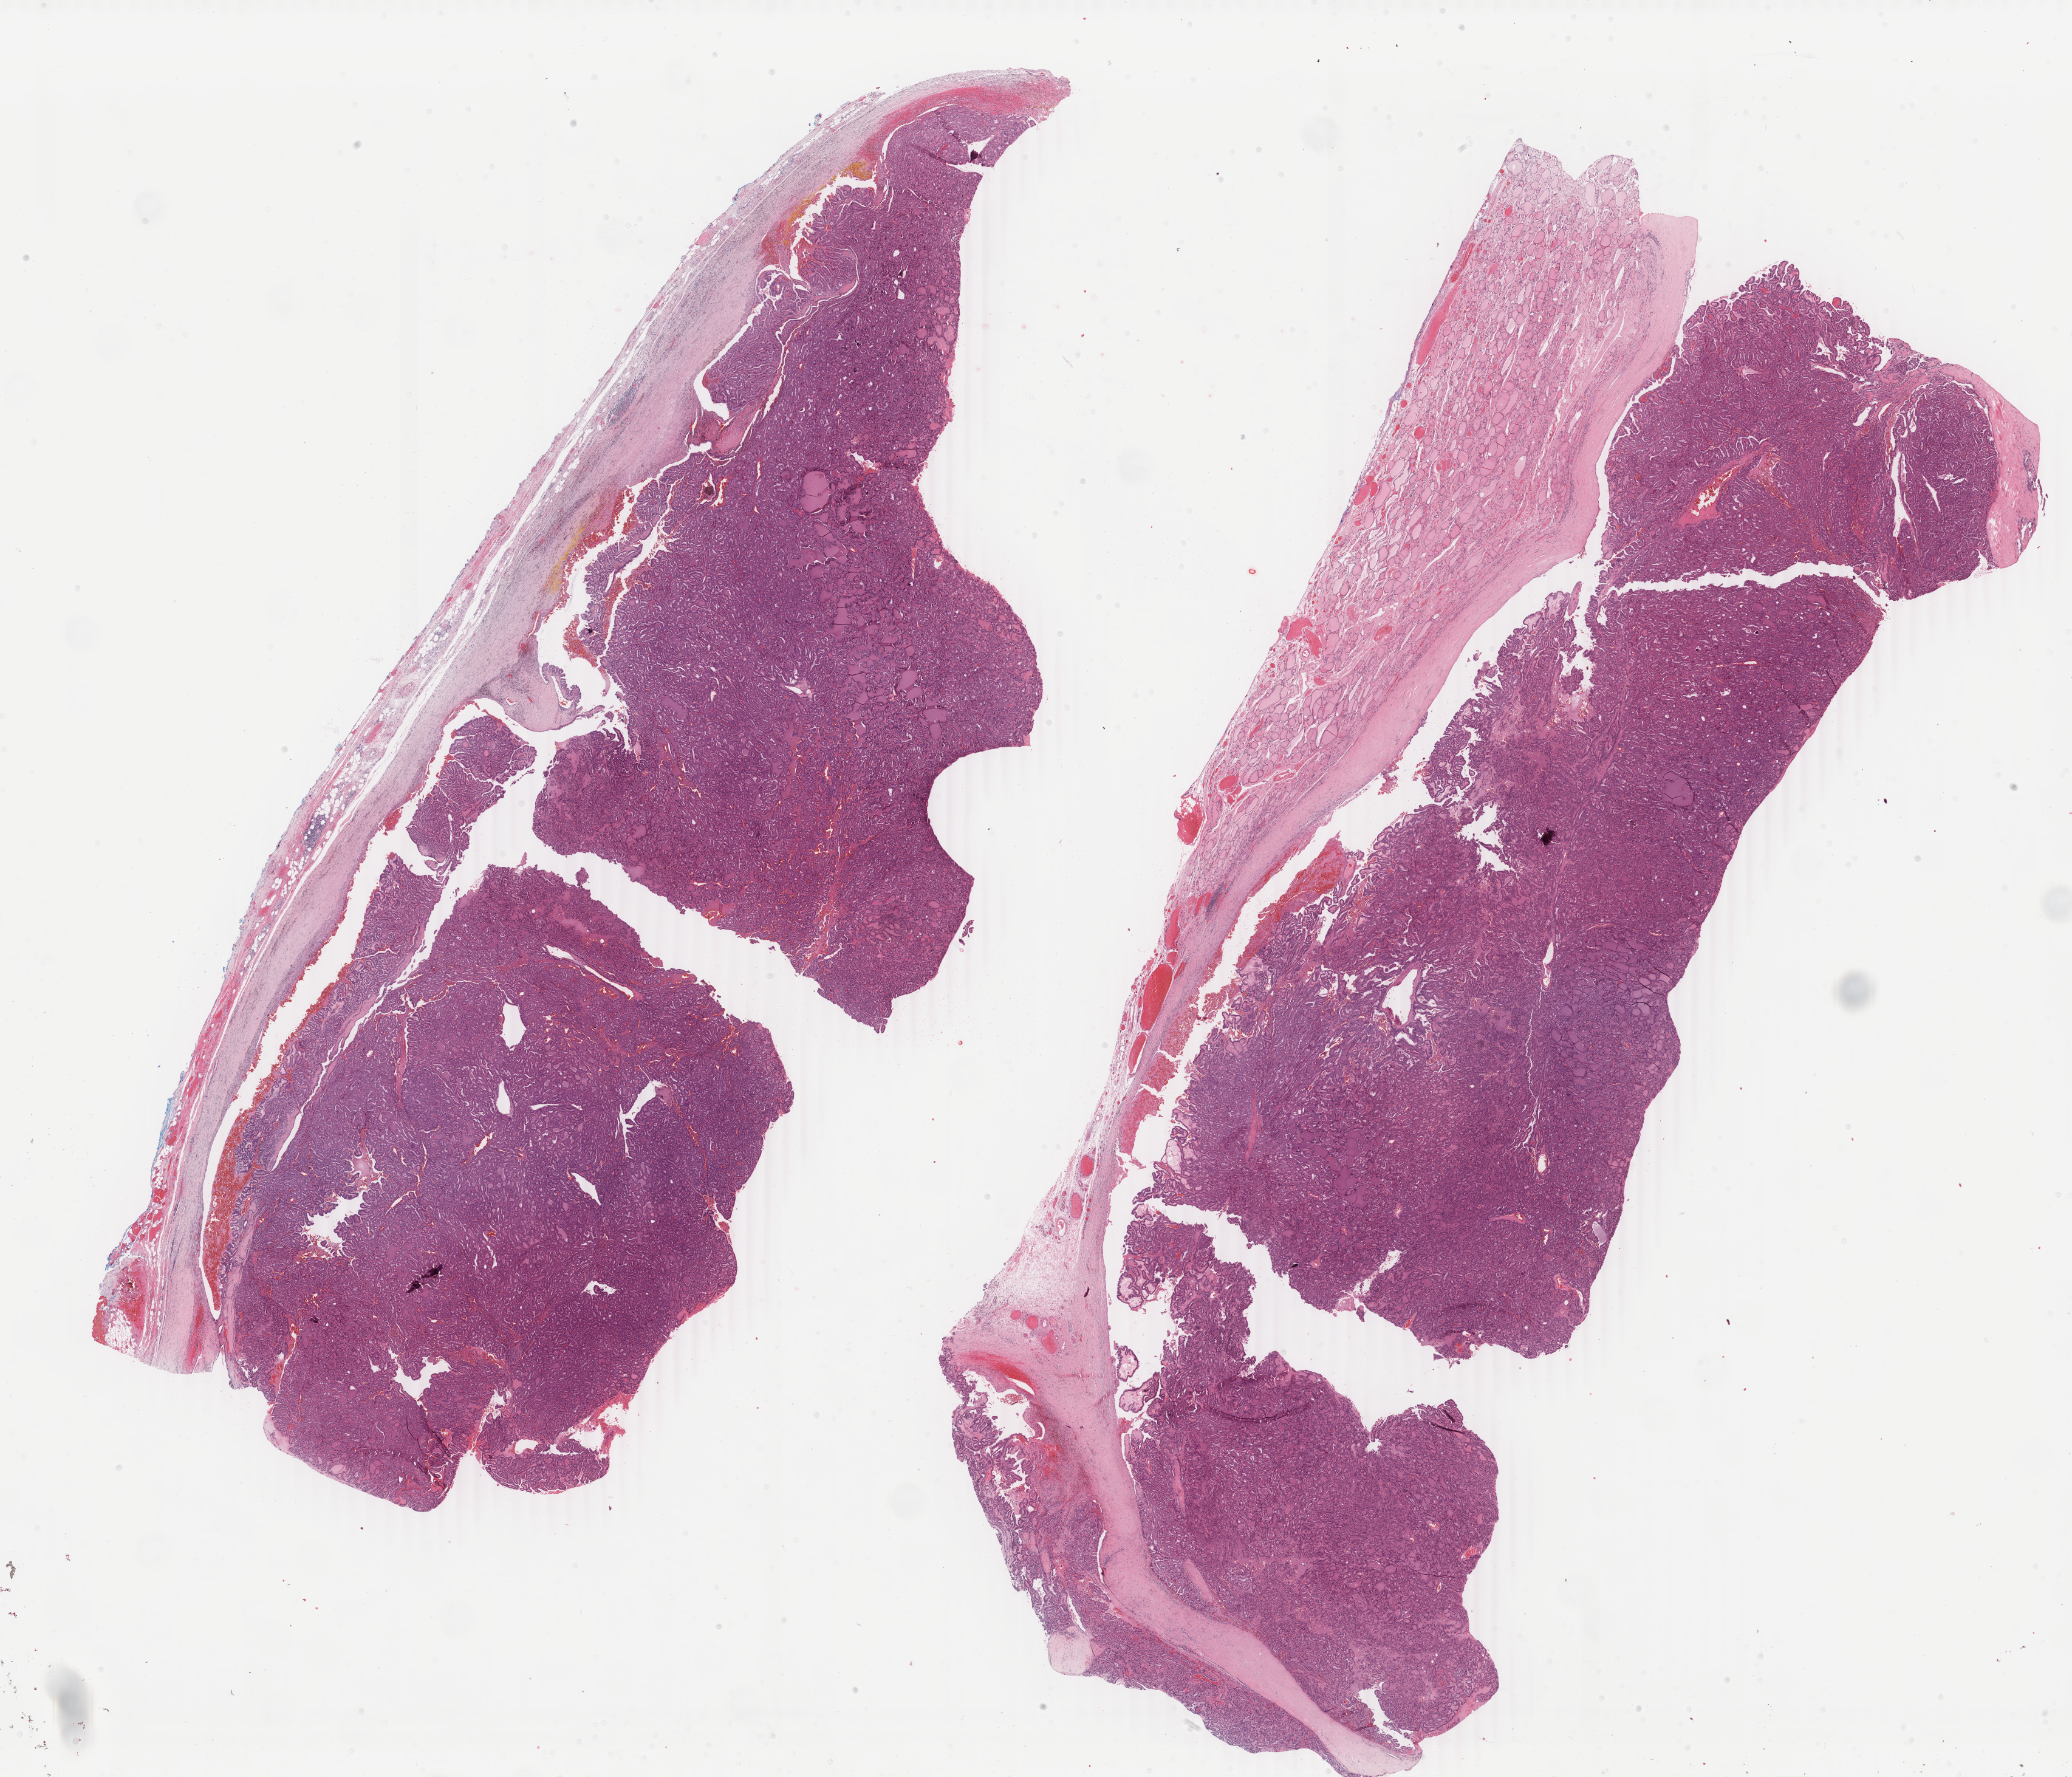
H&E whole-slide image, whole scanned area (about 27.1 x 23.3 mm, acquisition: 40x scan) shown as a low-resolution overview. Formalin-fixed paraffin-embedded (FFPE) diagnostic section. Thyroid, primary tumour sample. Patient: male, age at initial diagnosis 70 years.
* pathologic diagnosis: Papillary adenocarcinoma, NOS
* laterality: right
* lymph nodes positive (case pathology): 16 of 31 examined
* AJCC pathologic stage: IVA (7th edition)